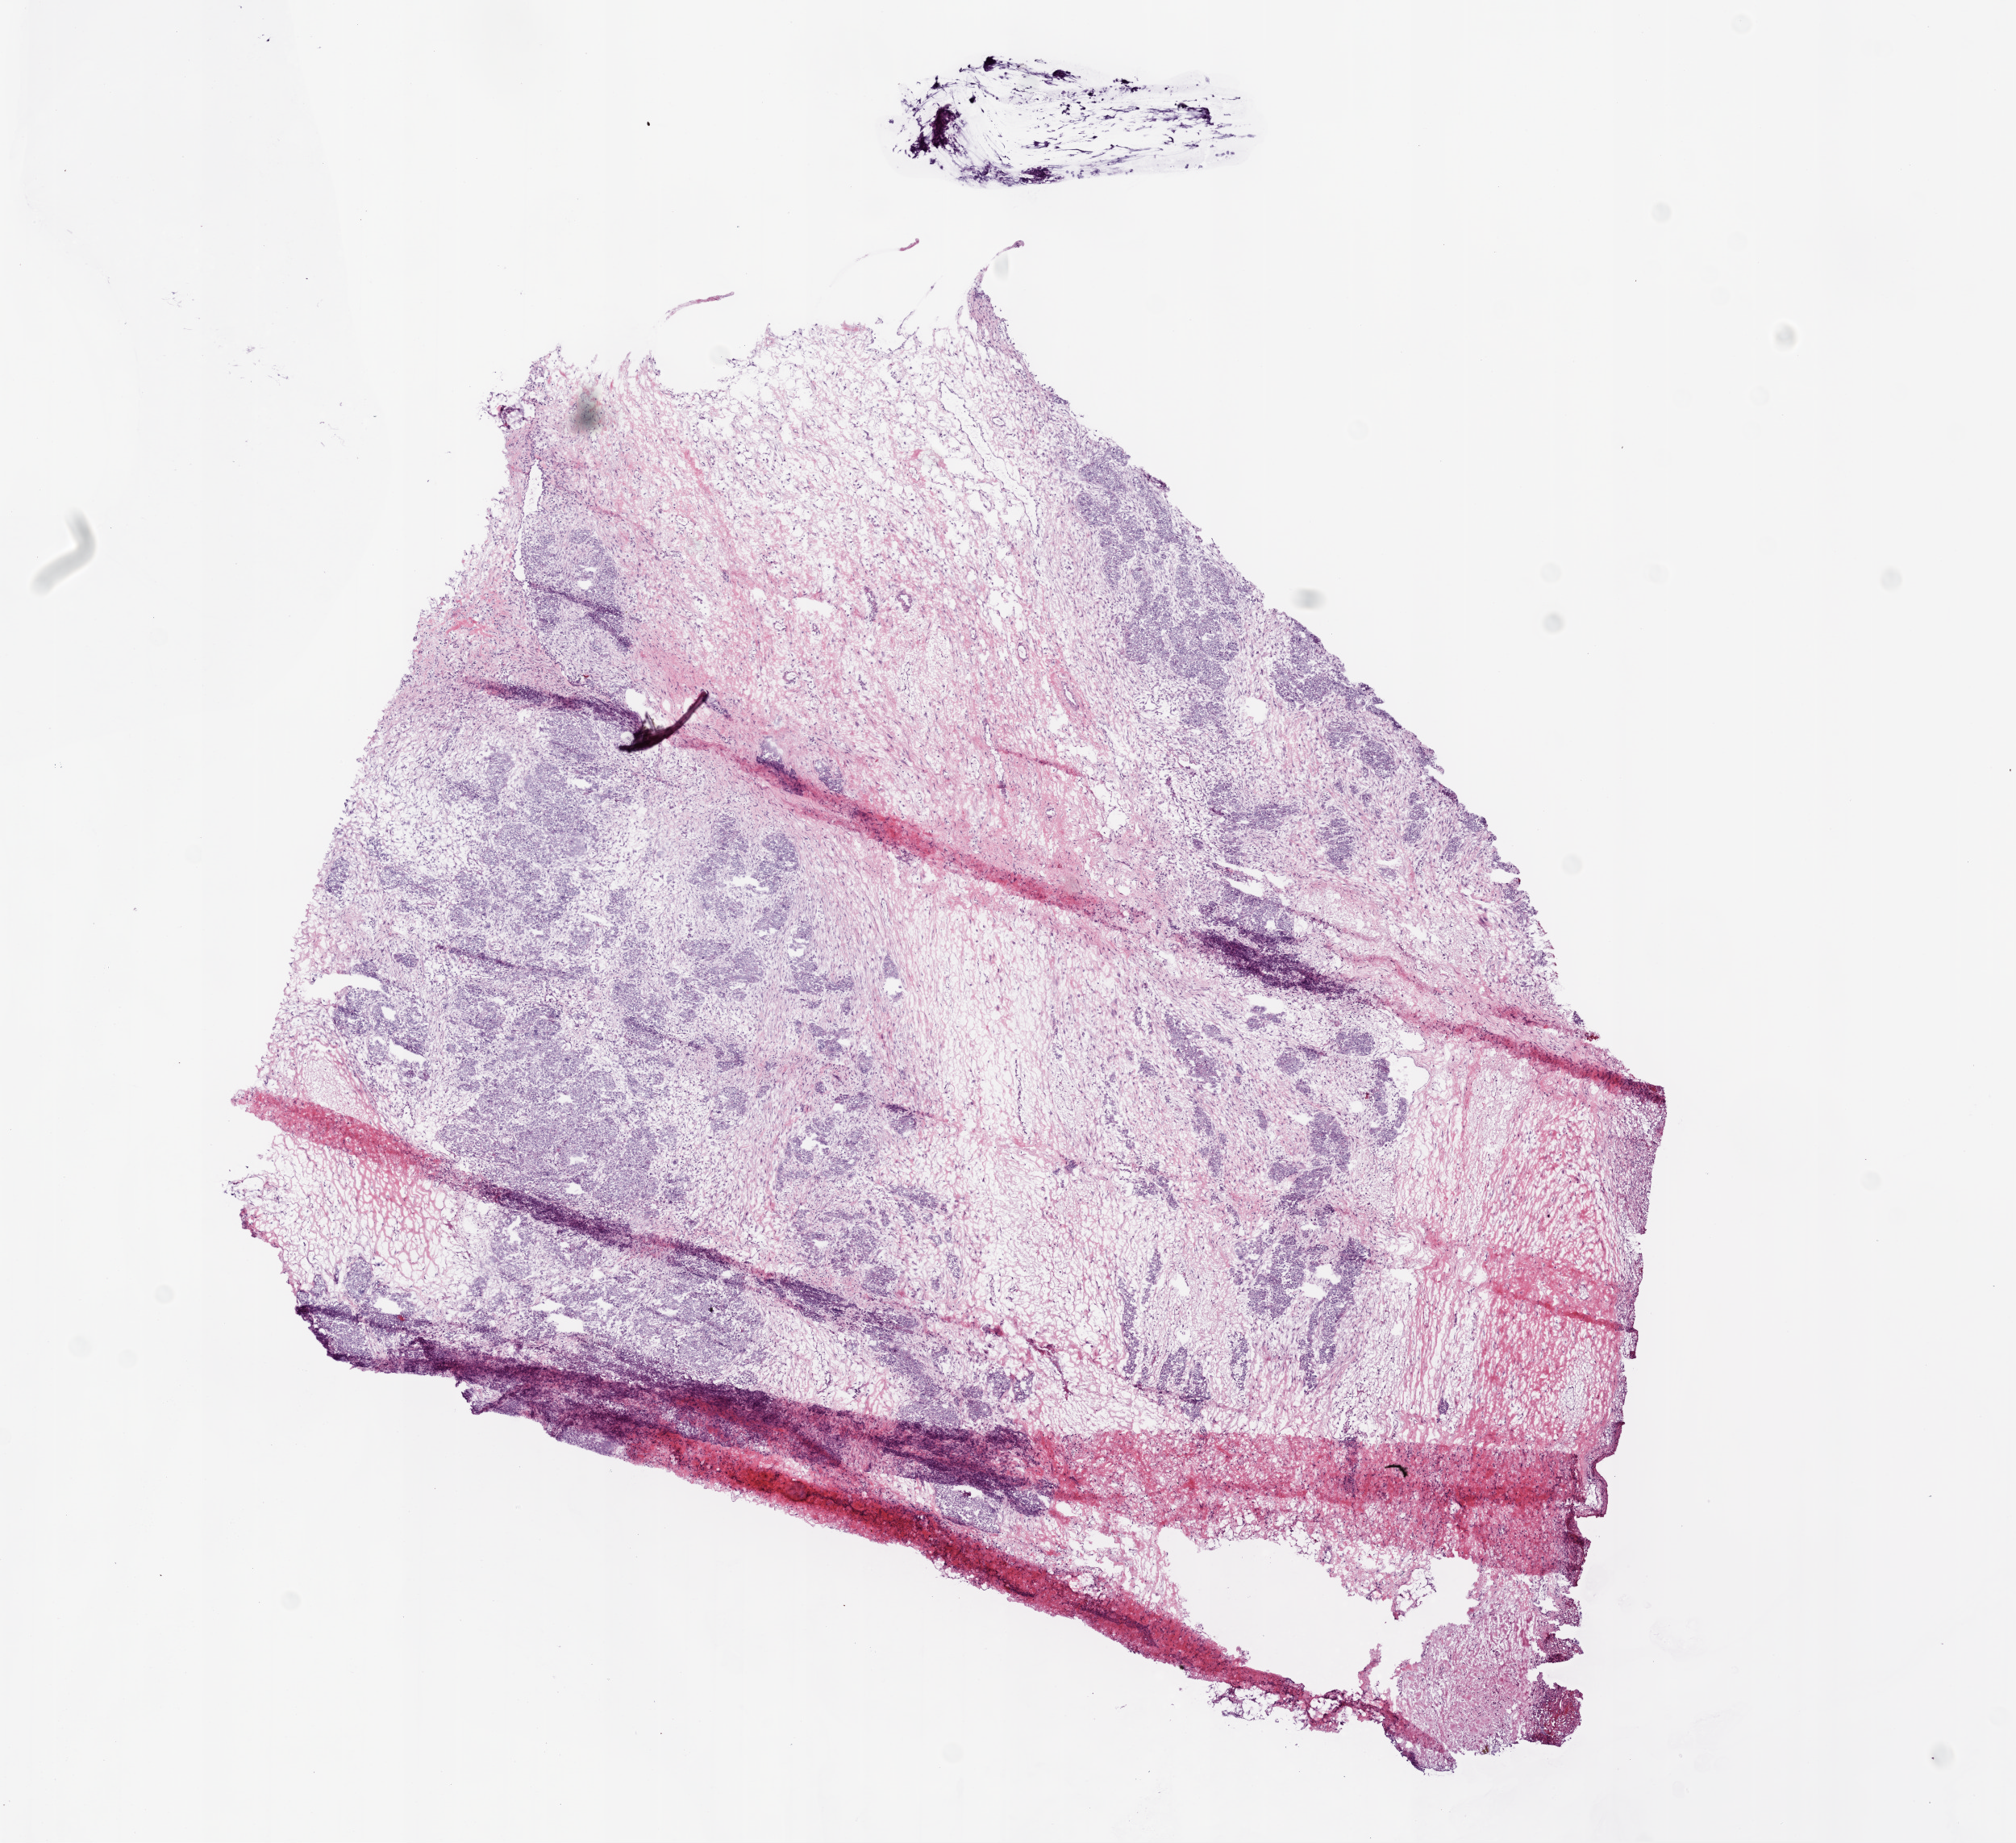
Whole-slide histology image, Hematoxylin and eosin (H&E) stained, shown as a low-resolution overview of the whole scanned area (about 10.0 x 9.2 mm, slide scanned at 20x). Frozen section from the top of the tissue portion. Ovary, primary tumour sample. Patient: female, age at initial diagnosis 60 years.
Pathologic diagnosis: Serous cystadenocarcinoma, NOS.